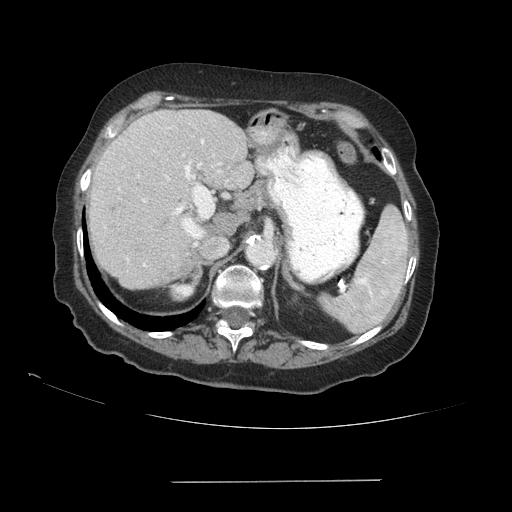
Contrast-enhanced abdominal CT (liver protocol), one axial slice; position 62 of 89 along the scan axis; reconstruction kernel STANDARD; 140 kVp; soft-tissue window (W 400 / L 40 HU); 2.5 mm slice thickness; 512 × 512 image matrix. From the clinical record (not read from this slice): diagnosis: hepatocellular carcinoma (patient treated with transarterial chemoembolisation; whether this scan precedes or follows treatment is not stated here); TNM stage (as recorded): Stage-IVA; Child-Pugh class: A; tumour differentiation: poorly differentiated; tumour nodularity: uninodular.
Annotated regions visible in this slice (semi-automatic segmentation, software-assisted and operator-edited):
- liver parenchyma outside the tumour (the mass and vessels are separate outlines, so this box may not span the whole liver): bounding box (x1, y1, x2, y2) in pixels: (88, 110, 252, 288)
- liver vessels: (118, 139, 220, 267)